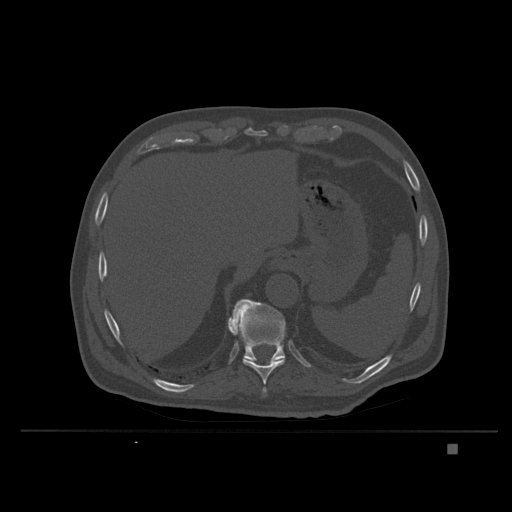
CT including the spine, one axial slice. Position 188 of 435 along the scan axis. Bone window (W 1800 / L 400 HU). 512 × 512 image matrix, field of view 434 × 434 mm. Patient: male, 73 years. From the clinical record (not read from this slice): primary cancer: skin.
Structures marked on this image (semi-automatically segmented with operator editing):
- T10 vertebra: bounding box <228,324,285,385> (left, top, right, bottom; pixels)
- T11 vertebra: <228,299,286,363>
- T9 vertebra: <262,387,267,397>